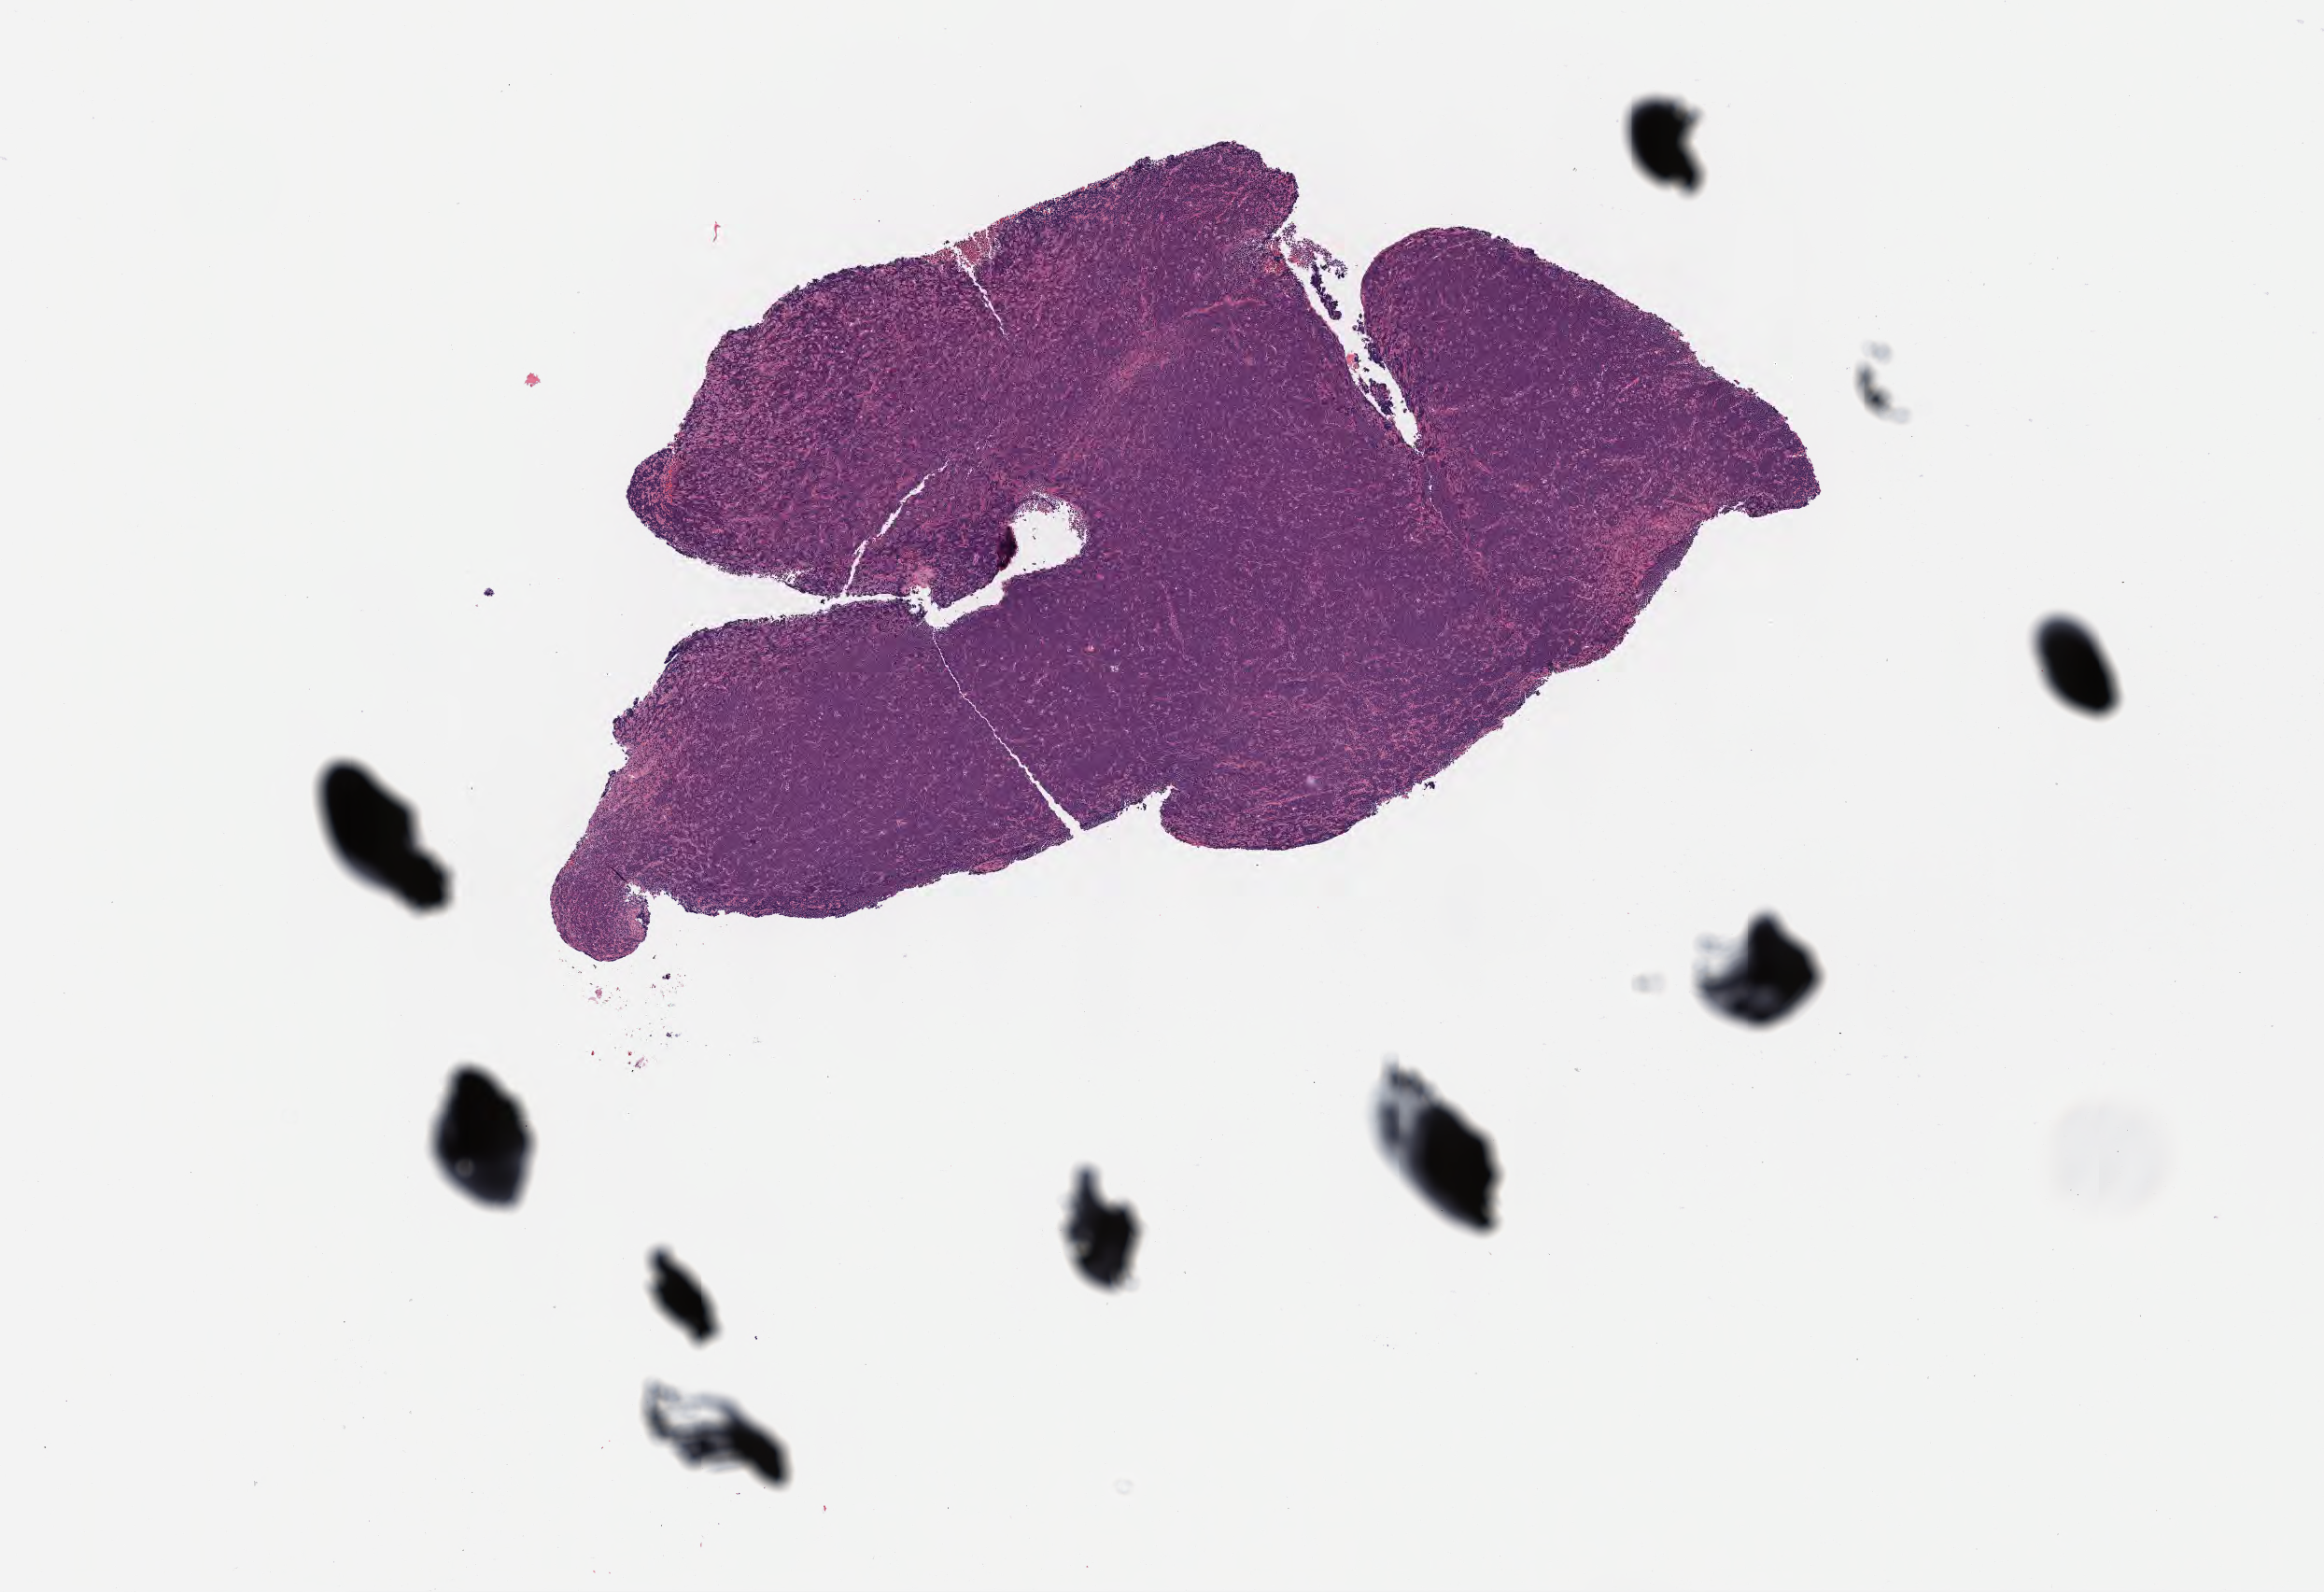
H&E whole-slide image, whole scanned area (about 10.1 x 6.9 mm) shown as a low-resolution overview, tumor tissue, site: buccal mucosa. Male patient; age at initial diagnosis 5 years.
Histologic diagnosis: Diffuse large B-cell lymphoma, NOS.